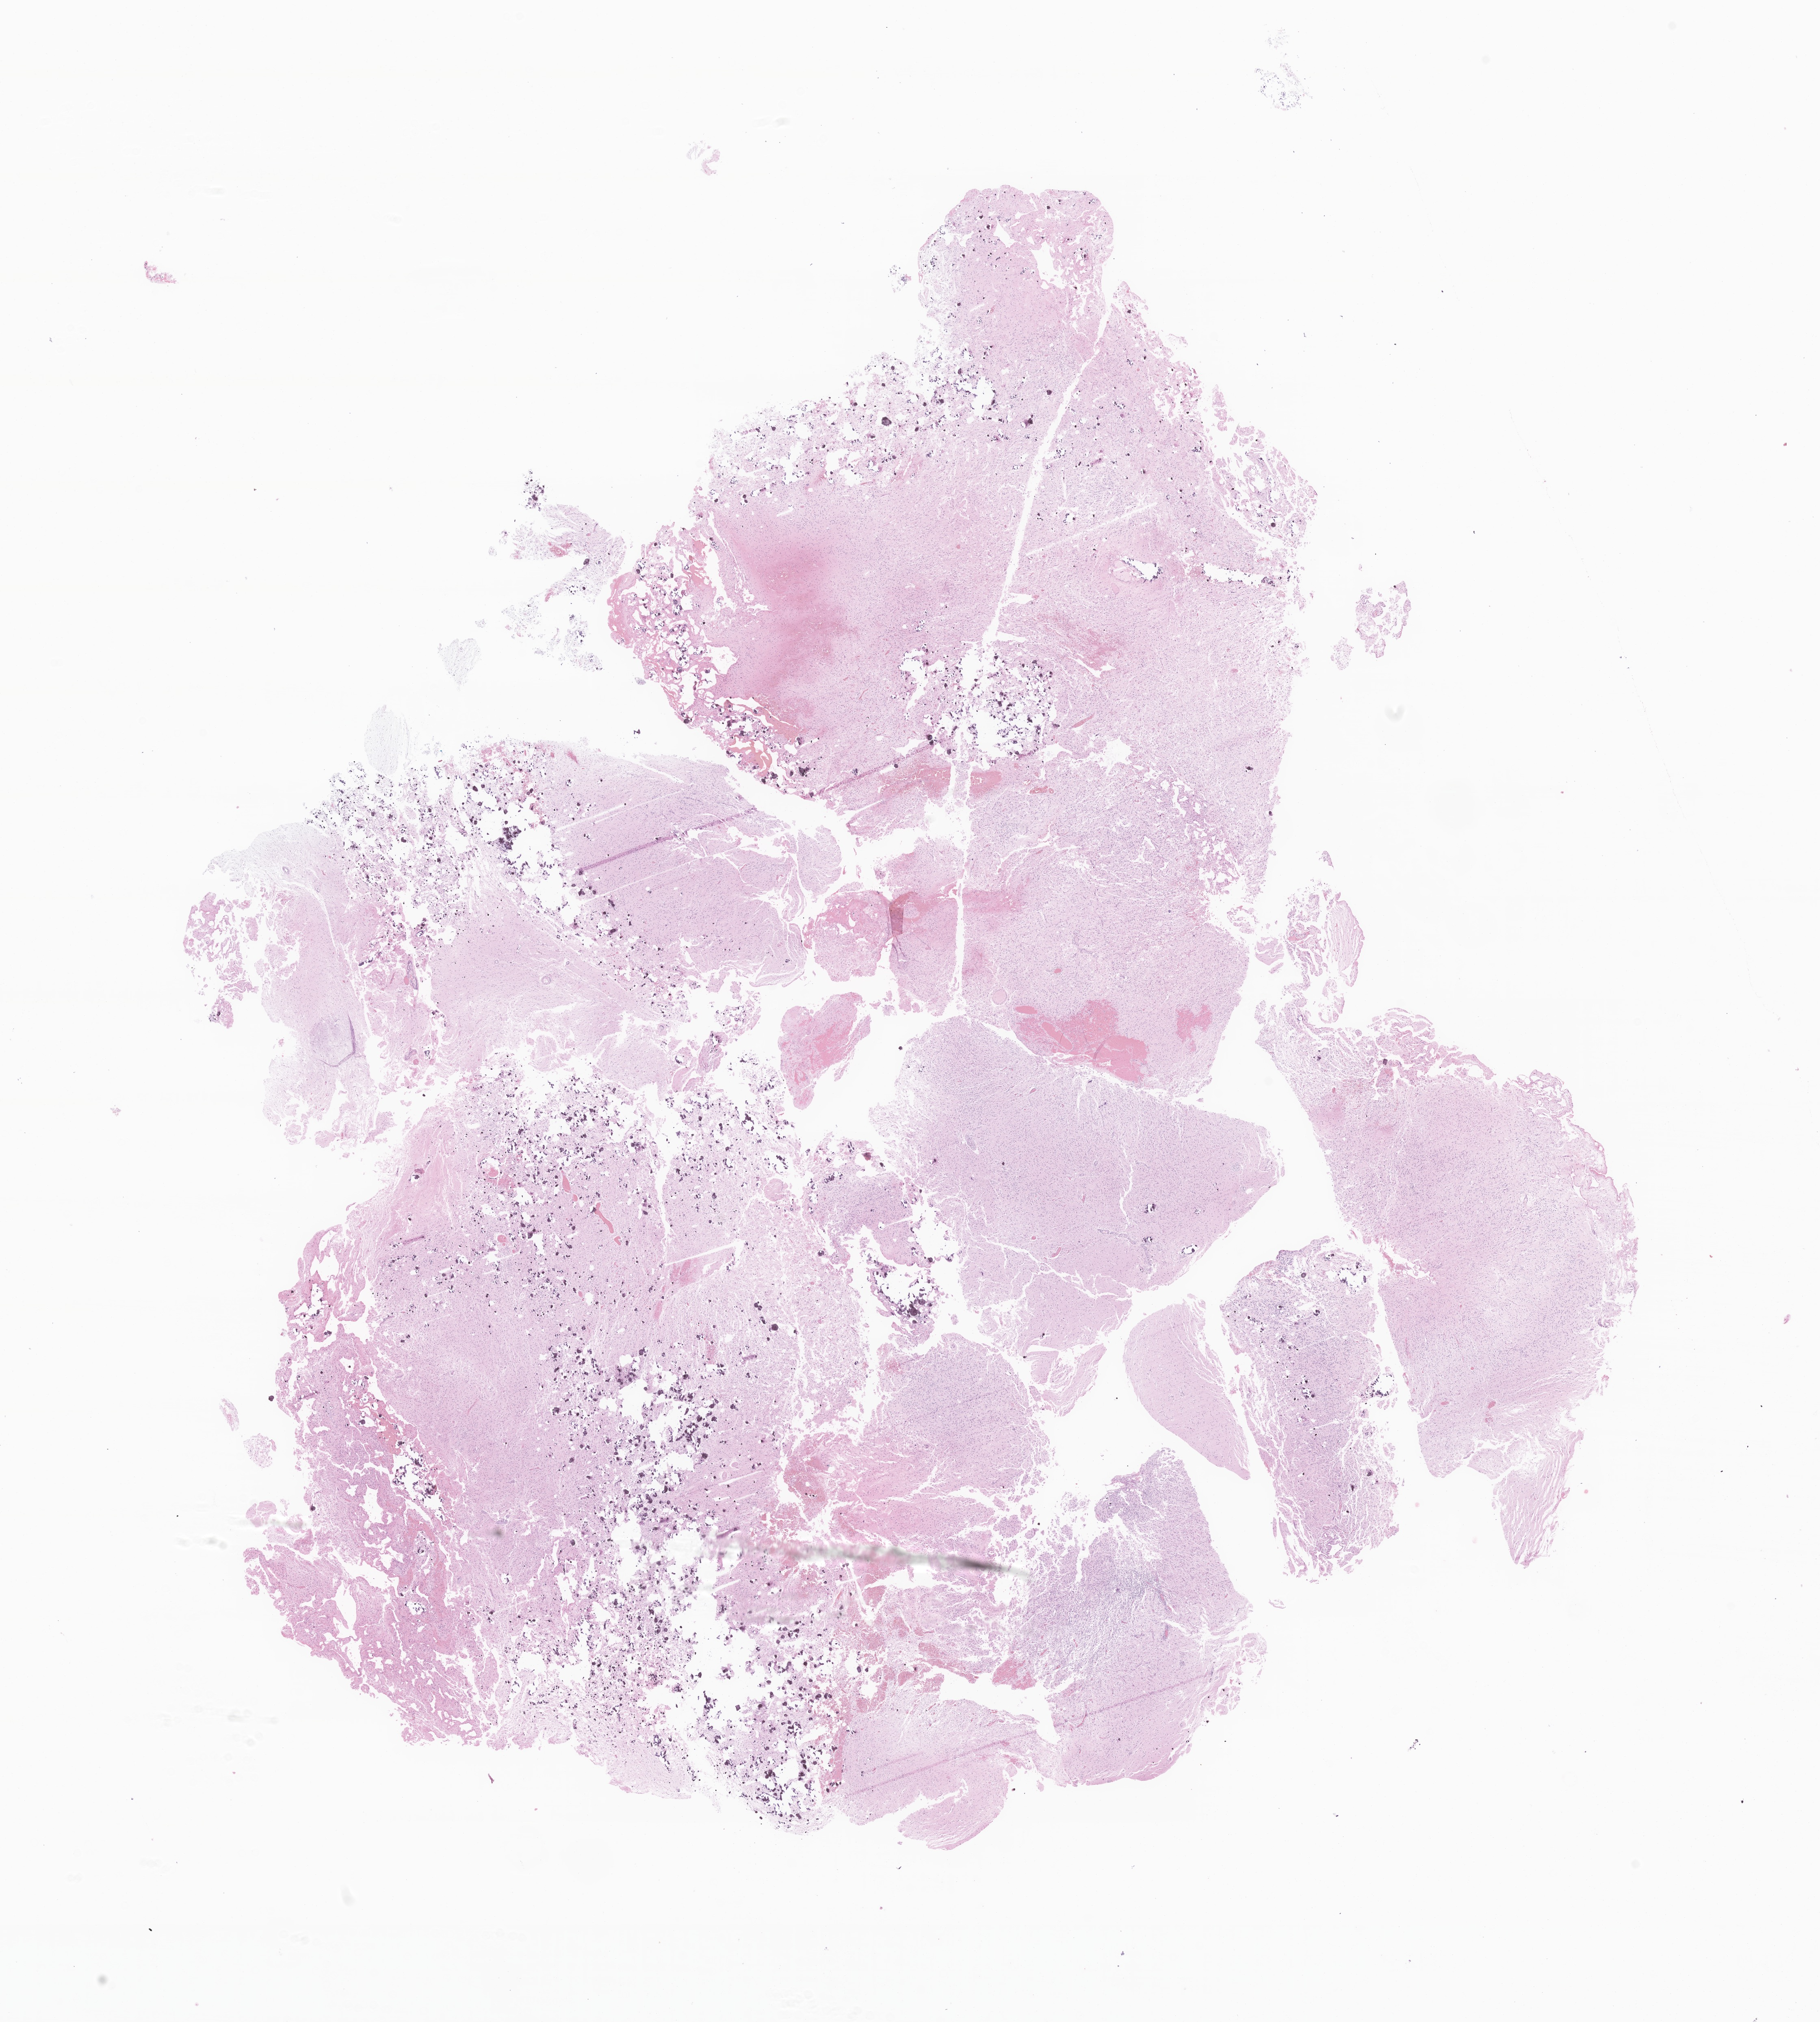
Whole-slide image, haematoxylin and eosin stain of tumor tissue from the brain — shown as a low-resolution overview of the whole scanned area (about 18.9 x 21.0 mm); formalin-fixed, paraffin-embedded (FFPE) tissue. Patient female; age 185 months (15 years 5 months).
Recorded diagnosis: Ganglioglioma, NOS.